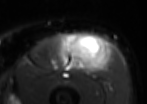
MRI of an extremity soft-tissue mass, one axial slice. Slice 42 of 85 in the series (ordered by position). T2-weighted fat-saturated. MR volume resampled by the dataset authors to the PET/CT grid (not the native acquisition matrix). 3.27 mm slice thickness. 147 × 104 image matrix. Male patient. From the clinical record (not read from this slice): histological type: extraskeletal osteosarcoma; grade: high; site of the primary tumour: thigh.
Structures marked on this image (expert contour drawn on MRI and transferred to this co-registered scan by the dataset authors):
- gross tumour volume (mass): bounding box [x1, y1, x2, y2] px = [60, 33, 105, 70]